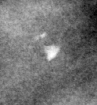
Cropped region of a digitized screen-film mammogram centred on a radiologist-marked abnormality; right breast; MLO view.
Finding: calcifications, morphology coarse; BI-RADS assessment category 2; benign without callback (not worked up further).